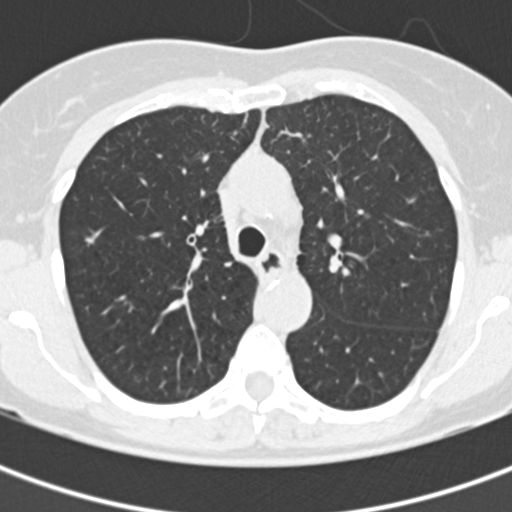
Low-dose screening chest CT, axial slice; first (baseline) screen; lung window (W 1500 / L -600 HU); 2 mm slice thickness; slice 61 of 177 in the series; 512 × 512 image matrix, field of view 280 × 280 mm. Female, age 60 years at enrolment. Current smoker at enrolment.
Expert-annotated lung lesion, bounding box <64,221,110,270> (left, top, right, bottom; pixels). No non-calcified nodule or mass ≥4 mm was recorded by the screening reader at this exam. Official screen result: negative screen, no significant abnormalities. Participant outcome: lung cancer diagnosed 861 days after this screen — bronchiolo-alveolar adenocarcinoma, NOS, right upper lobe, well differentiated (G1), stage IA (AJCC 6th edition), 11 mm at pathology.